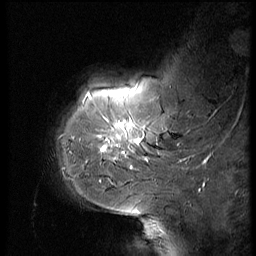
Breast MRI (dynamic contrast-enhanced), one sagittal slice; dynamic contrast-enhanced series, image 2 of 3 at this slice position (ordered by acquisition); 1.5 T; TE 4.2 ms, TR 9 ms; 2.5 mm slice thickness; 256 × 256 image matrix. Female patient, age 61 years. From the clinical record (not read from this slice): setting: breast cancer imaged before/during neoadjuvant chemotherapy; receptor status: HR-positive, HER2-negative.
Structures marked on this image (semi-automatically segmented with operator editing):
- analysis volume of interest (the breast-tissue region the enhancement analysis was run in; not a lesion): bounding box (x1, y1, x2, y2) in pixels: (65, 74, 185, 175)
- tumour enhancement mask (voxels above the 140 % enhancement threshold inside the analysis volume of interest): (101, 121, 148, 161)